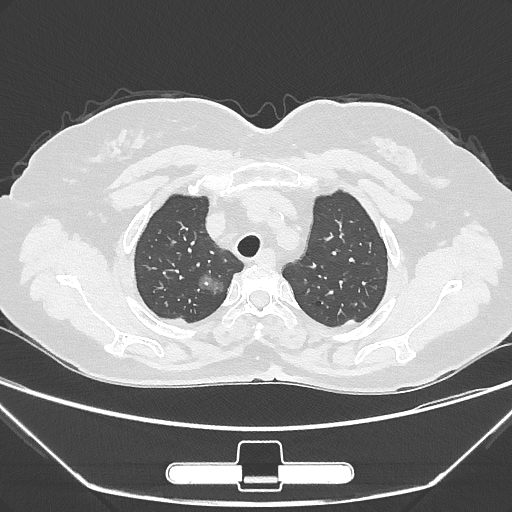
Chest CT, one axial slice. Slice 231 of 275 in the series (ordered by position). Reconstruction kernel IMR1,SharpPlus. 120 kVp. Lung window (W 1500 / L -600 HU). 1 mm slice thickness. 512 × 512 image matrix. Patient: female, 63 years. From the clinical record (not read from this slice): clinical TNM (as recorded): T1a N0 M0; histopathological grade: G1.
Annotated regions visible in this slice (bounding box drawn by a radiologist):
- lung tumour (recorded histology: adenocarcinoma): bounding box <195,273,234,304> (left, top, right, bottom; pixels)